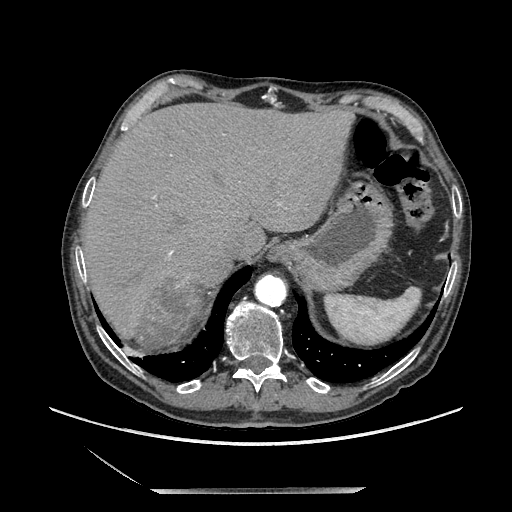
Contrast-enhanced abdominal CT, one axial slice. Slice 174 of 243 in the series (ordered by position). Soft-tissue window (W 400 / L 40 HU). 1.25 mm slice thickness. 512 × 512 image matrix, field of view 420 × 420 mm. Male patient. From the clinical record (not read from this slice): diagnosis: adrenocortical carcinoma; tumour side: right adrenal; tumour size at pathology: 16 cm; Ki-67 index: 17 %; stage (as recorded): 3.
Outlined on this slice (semi-automatic segmentation, software-assisted and operator-edited):
- mass: bounding box [x1, y1, x2, y2] px = [135, 280, 205, 350]